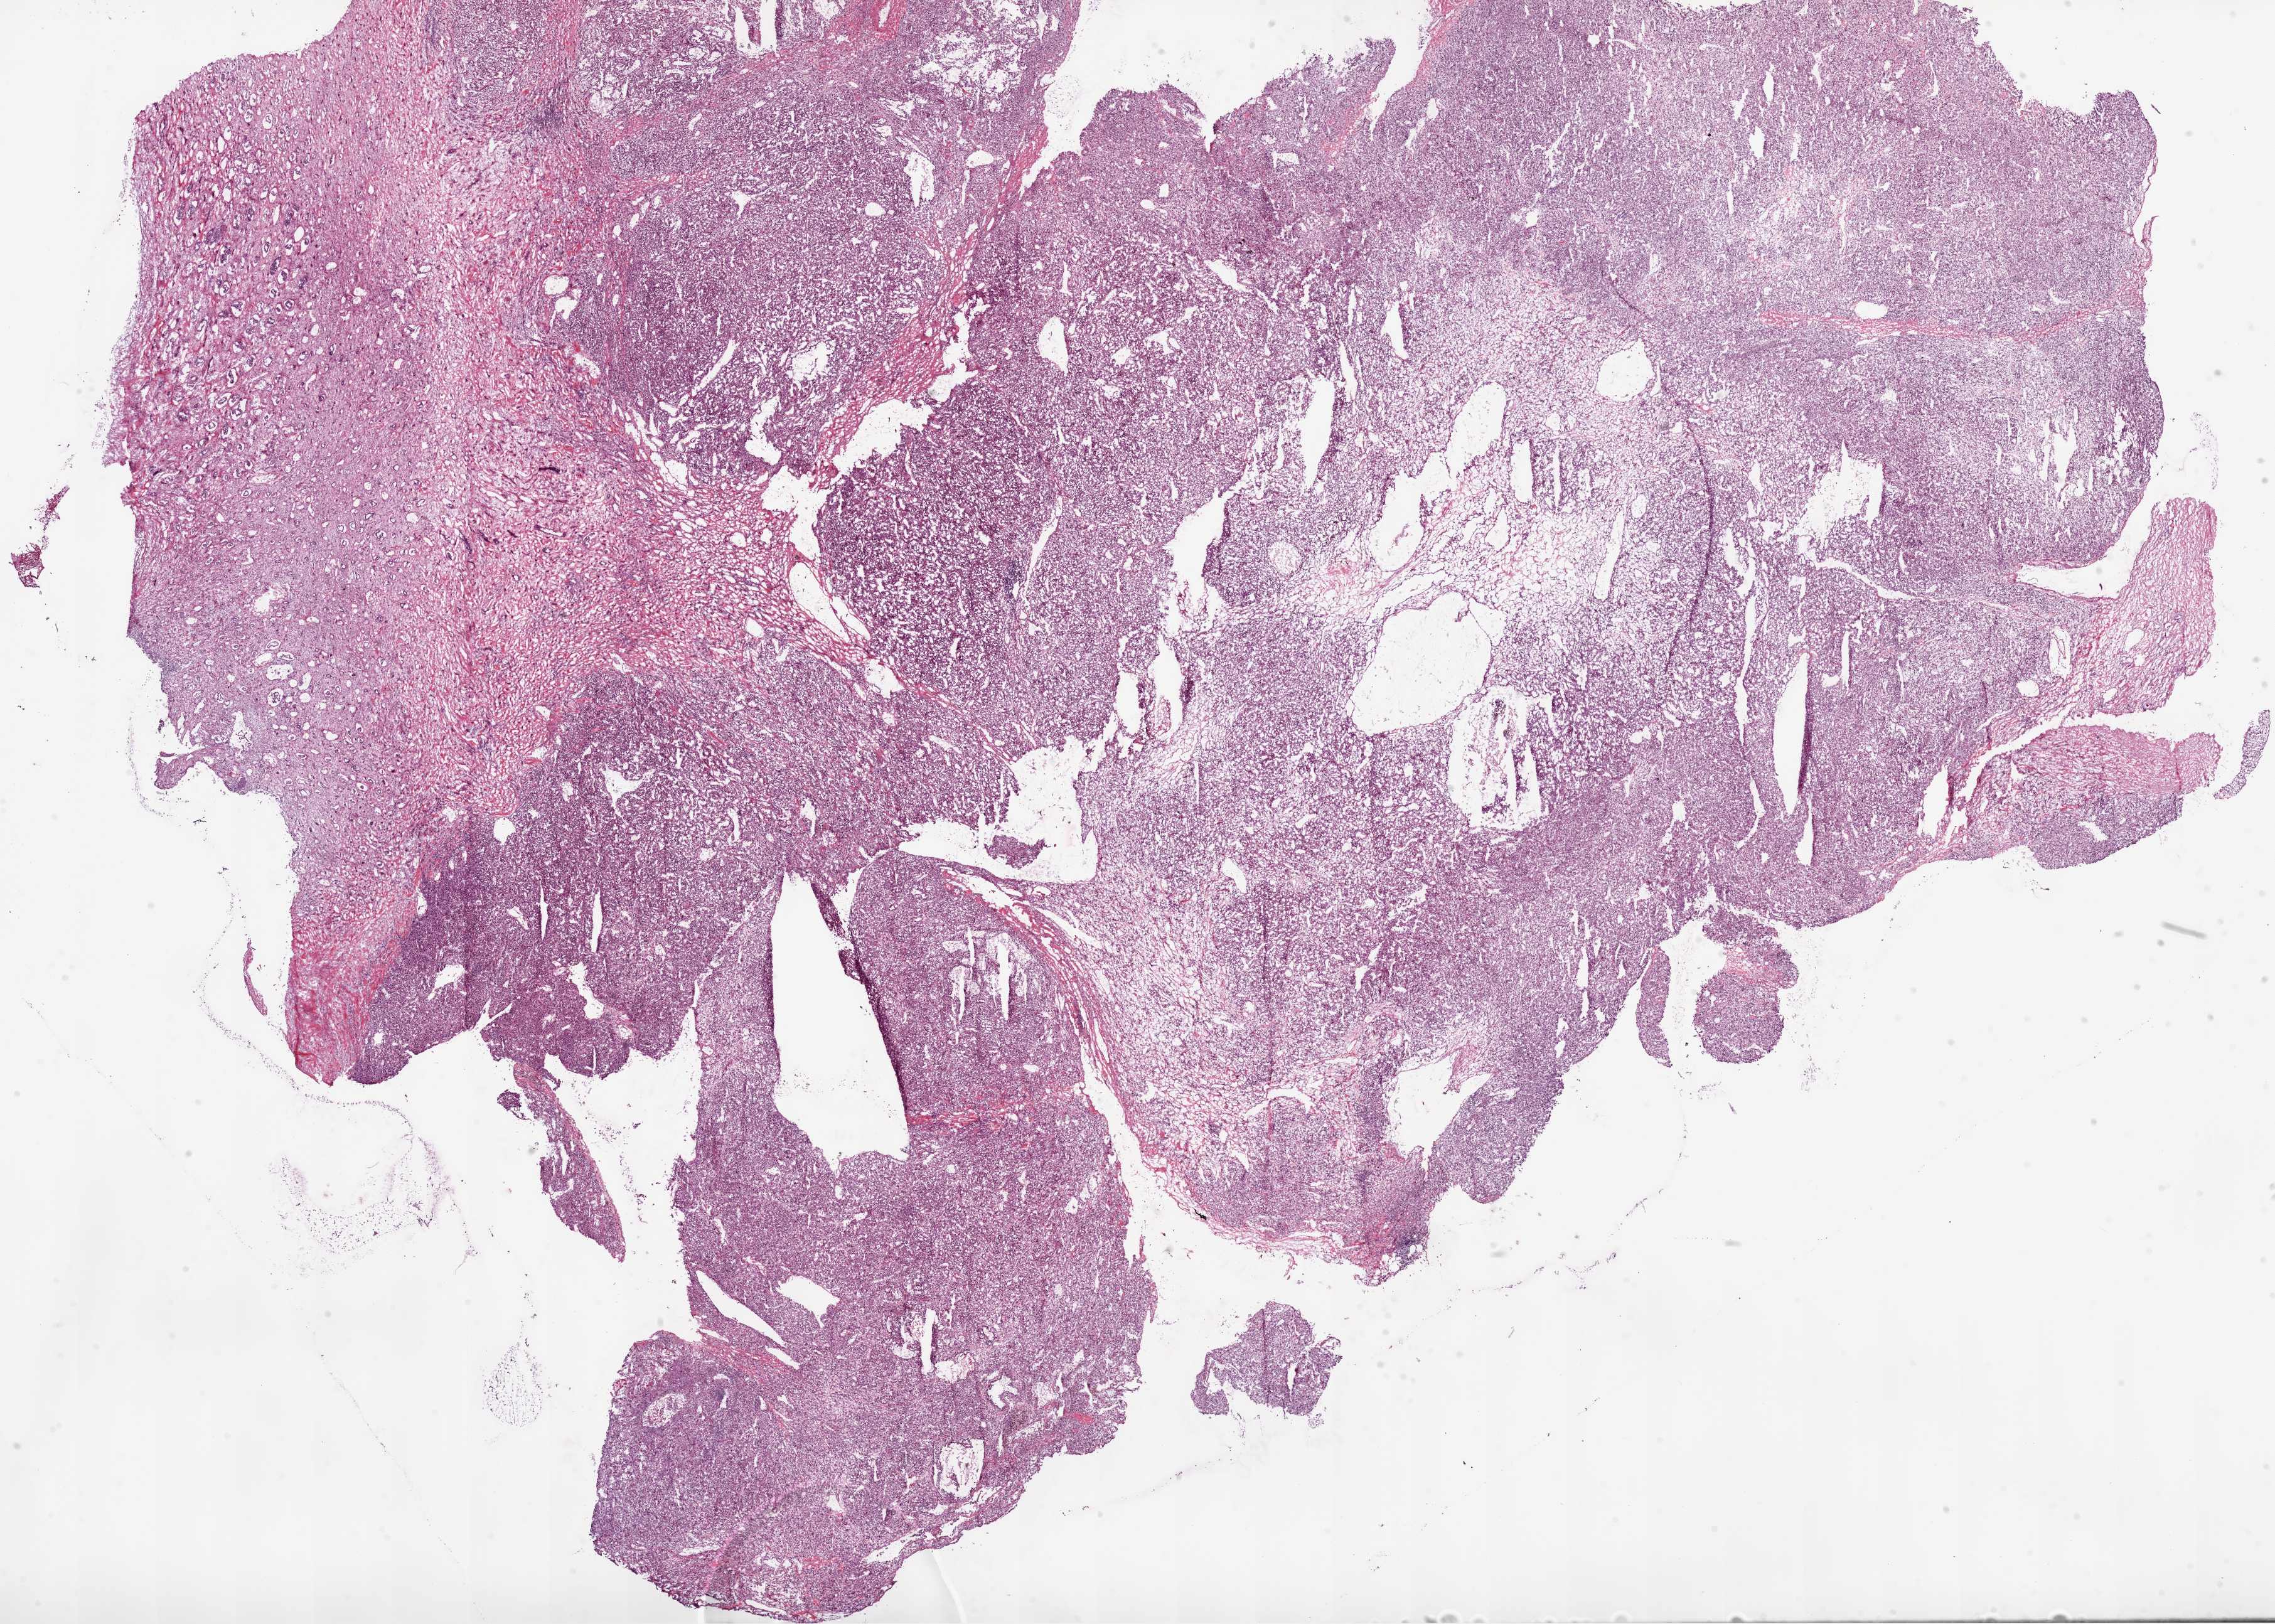
H&E whole-slide image — a low-resolution overview of the entire scanned area, about 29.1 x 20.8 mm. Frozen section from the bottom of the tissue portion. Sample: primary tumour, kidney. Male, age 48 years at initial diagnosis. Histologic grade: G3 (poorly differentiated). Slide review estimates, as recorded: tumour cells 70%, tumour nuclei 75%, normal cells 20%, stromal cells 10%, necrosis 0%.
• lymph nodes positive (case pathology): 0 of 3 examined
• histologic diagnosis: Clear cell adenocarcinoma, NOS
• laterality: left
• AJCC pathologic stage: III (5th edition)